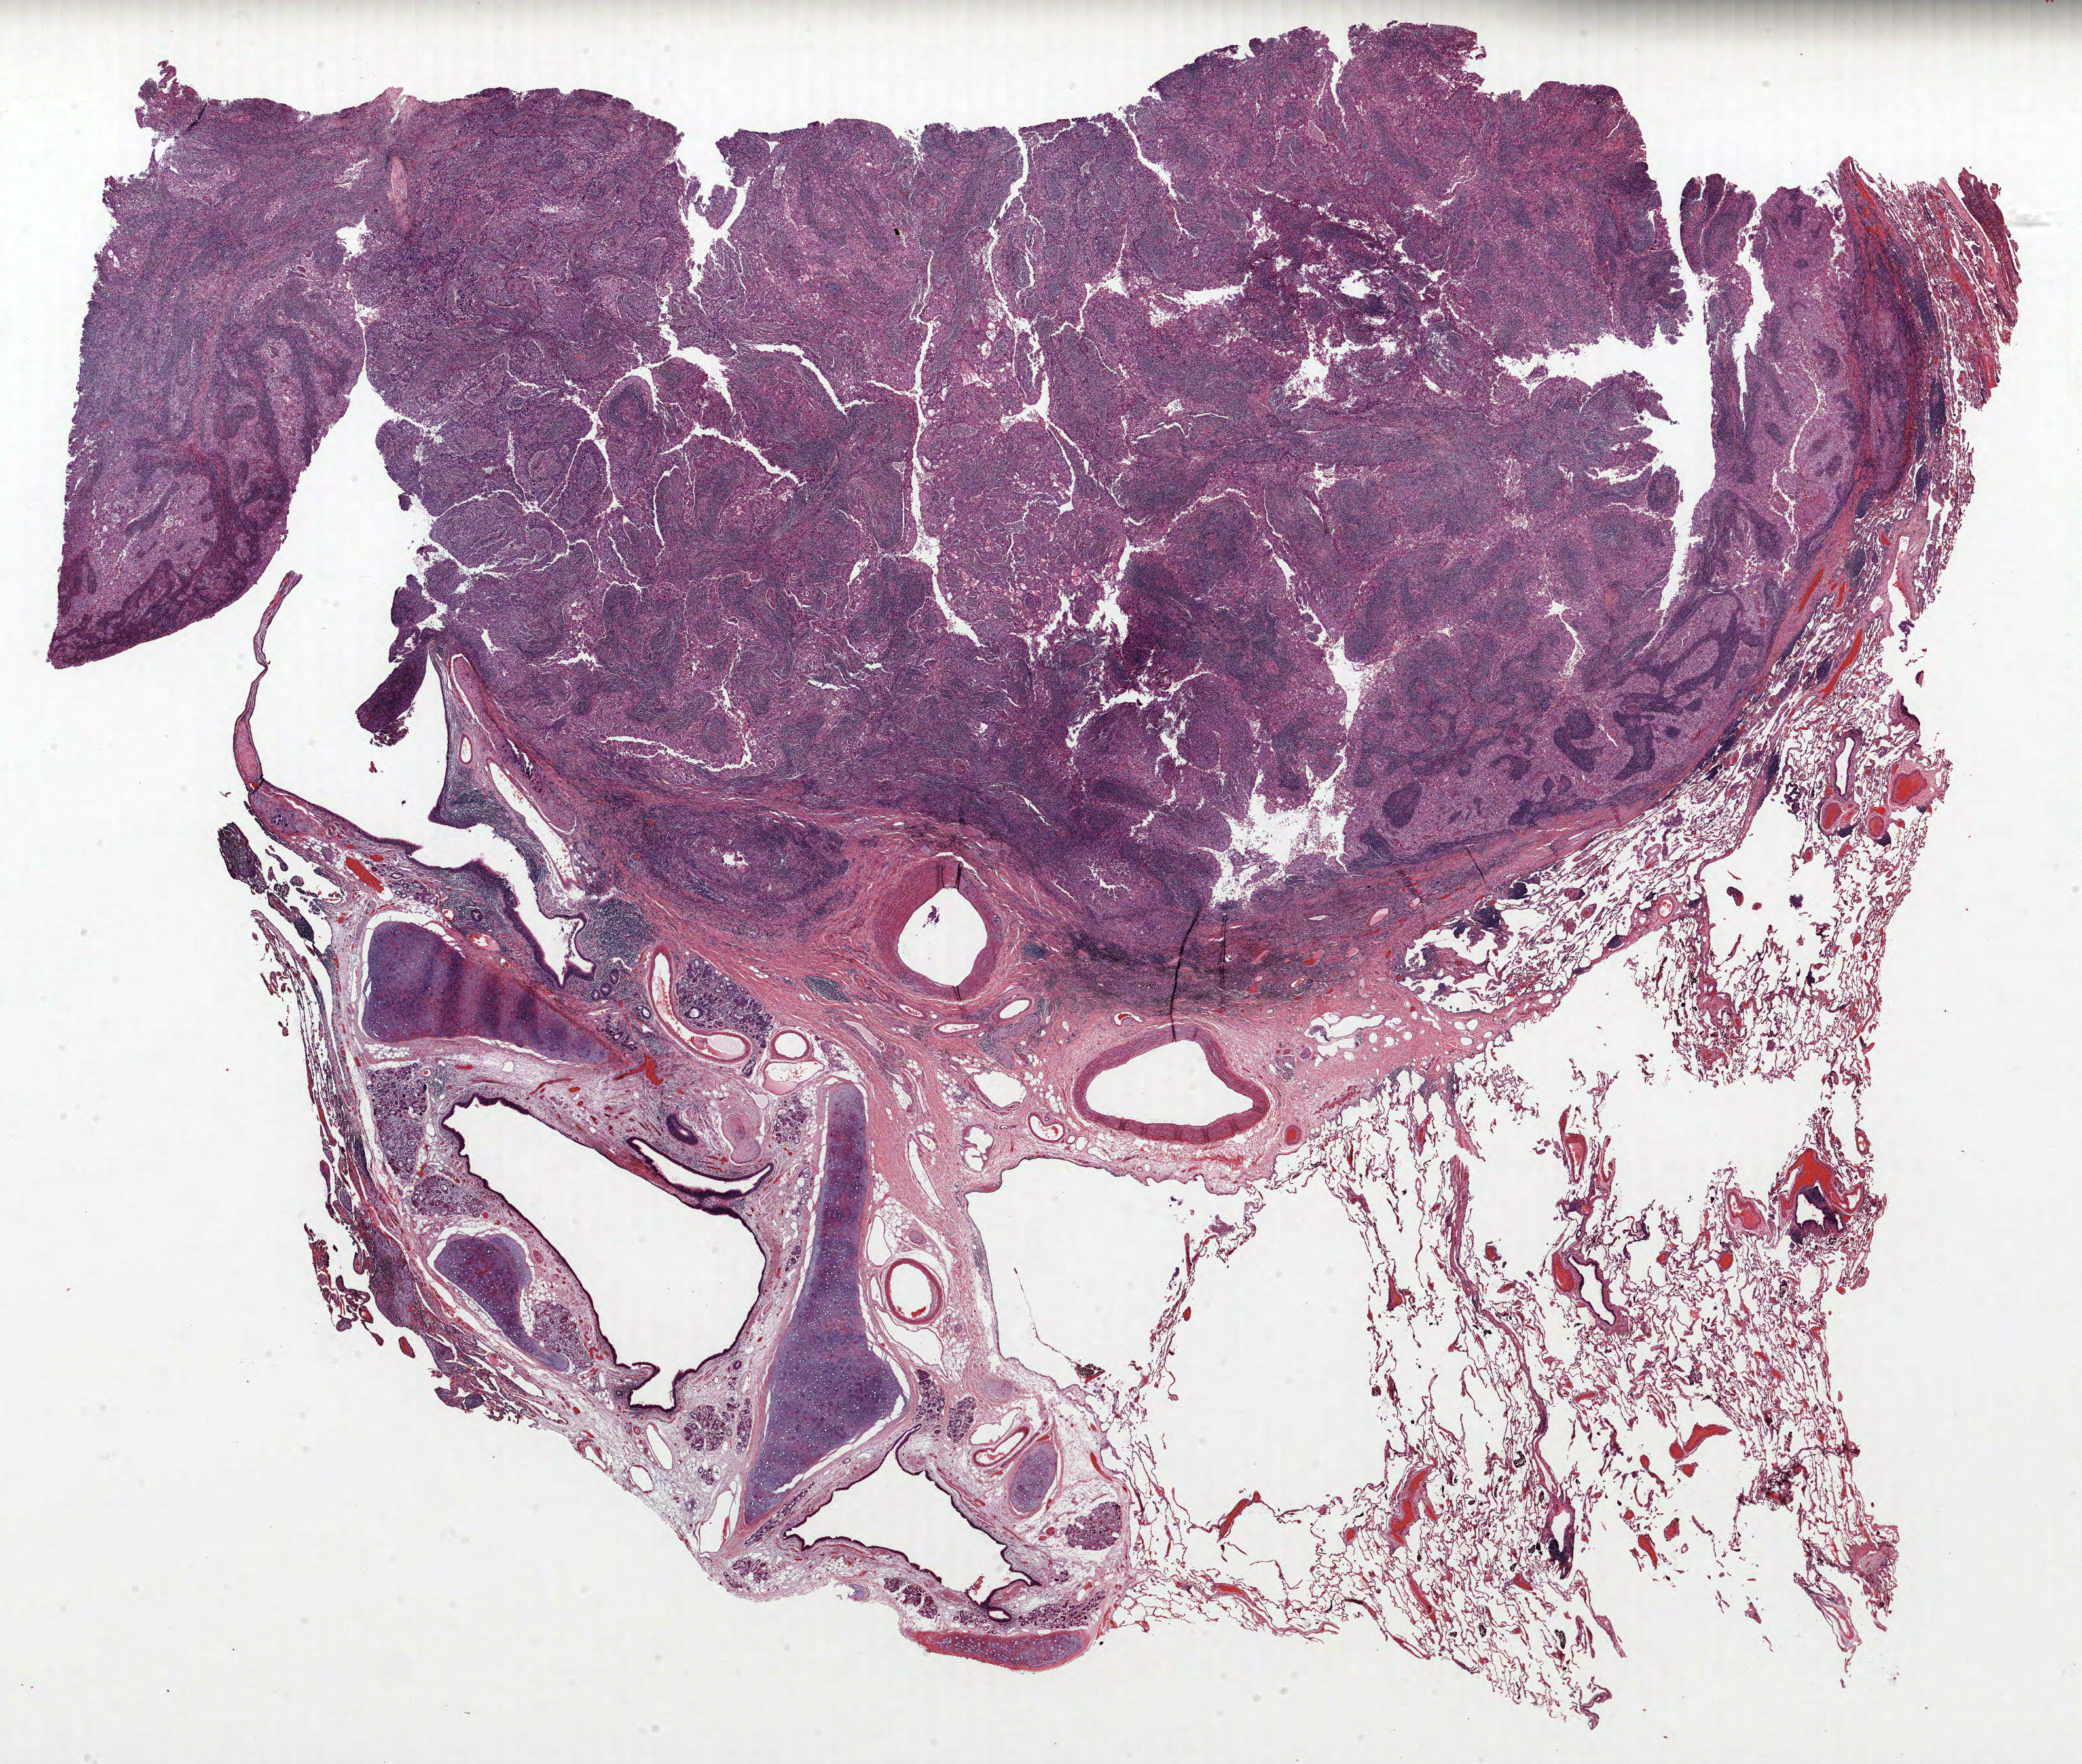
H&E-stained whole-slide image — shown as a low-resolution overview of the whole scanned area (about 25.4 x 21.6 mm, acquisition: 40x scan), formalin-fixed paraffin-embedded (FFPE) section, lung. Male patient, aged 70 at enrolment. Former smoker at enrolment. Grade: poorly differentiated (G3).
- stage (AJCC 6th edition): IIIA
- participant's lung-cancer diagnosis: Adenocarcinoma, NOS (ICD-O-3 8140/3)
- ICD-O-3 topography: upper lobe of lung (C34.1)
- tumour size (pathology): 50 mm
- primary tumour location (clinical record): right upper lobe